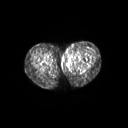
FDG PET of an extremity soft-tissue mass (from a PET/CT study), one axial slice. Slice 40 of 267 in the series (ordered by position). 128 × 128 image matrix, field of view 600 × 600 mm. Female patient, age 24 years. From the clinical record (not read from this slice): histological type: leiomyosarcoma; grade: high; site of the primary tumour: groin.
Outlined on this slice (expert contour drawn on MRI and transferred to this co-registered scan by the dataset authors):
- gross tumour volume including surrounding oedema: box from (x=61, y=50) to (x=79, y=65) px